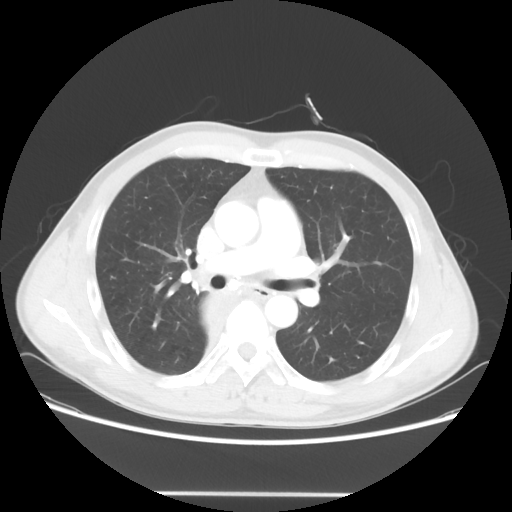
Chest CT, one axial slice. Slice 37 of 62 in the series (ordered by position). 120 kVp. Lung window (W 1500 / L -600 HU). 5 mm slice thickness. 512 × 512 image matrix, field of view 393 × 393 mm. Male patient, age 47 years. From the clinical record (not read from this slice): clinical TNM (as recorded): T2 N0 M0.
Outlined on this slice (bounding box drawn by a radiologist):
- lung tumour (recorded histology: squamous cell carcinoma): bounding box <195,283,231,340> (left, top, right, bottom; pixels)